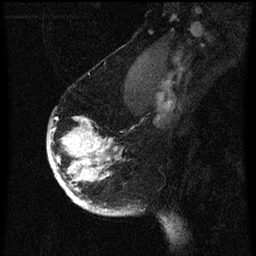
Breast MRI (dynamic contrast-enhanced), one sagittal slice. Position 46 of 60 along the scan axis. Dynamic contrast-enhanced series, image 2 of 3 at this slice position (ordered by acquisition). 1.5 T. TE 4.2 ms, TR 8 ms. 256 × 256 image matrix. Patient: female, 56 years.
Annotated regions visible in this slice (semi-automatically segmented with operator editing):
- analysis volume of interest (the breast-tissue region the enhancement analysis was run in; not a lesion): bounding box (x1, y1, x2, y2) in pixels: (48, 118, 125, 217)
- tumour enhancement mask (voxels above the 70 % enhancement threshold inside the analysis volume of interest): (48, 118, 123, 215)